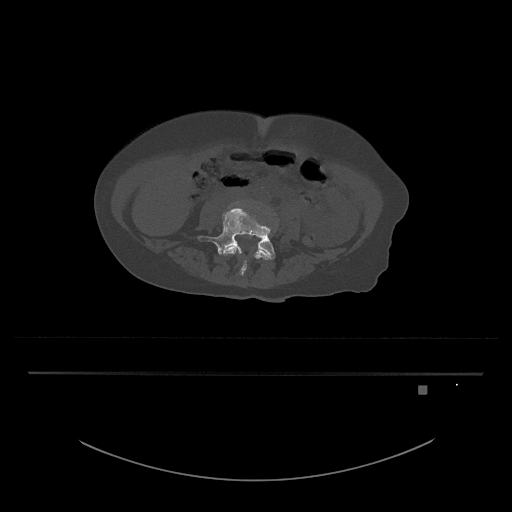
CT including the spine, one axial slice. Position 327 of 797 along the scan axis. 120 kVp. Bone window (W 1800 / L 400 HU). 0.5 mm slice thickness. 512 × 512 image matrix, field of view 500 × 500 mm. Patient: female, 57 years. Case-level facts recorded for this patient, not image findings: primary cancer: cervical.
Outlined on this slice (semi-automatically segmented with operator editing):
- L4 vertebra: box from (x=223, y=246) to (x=271, y=277) px